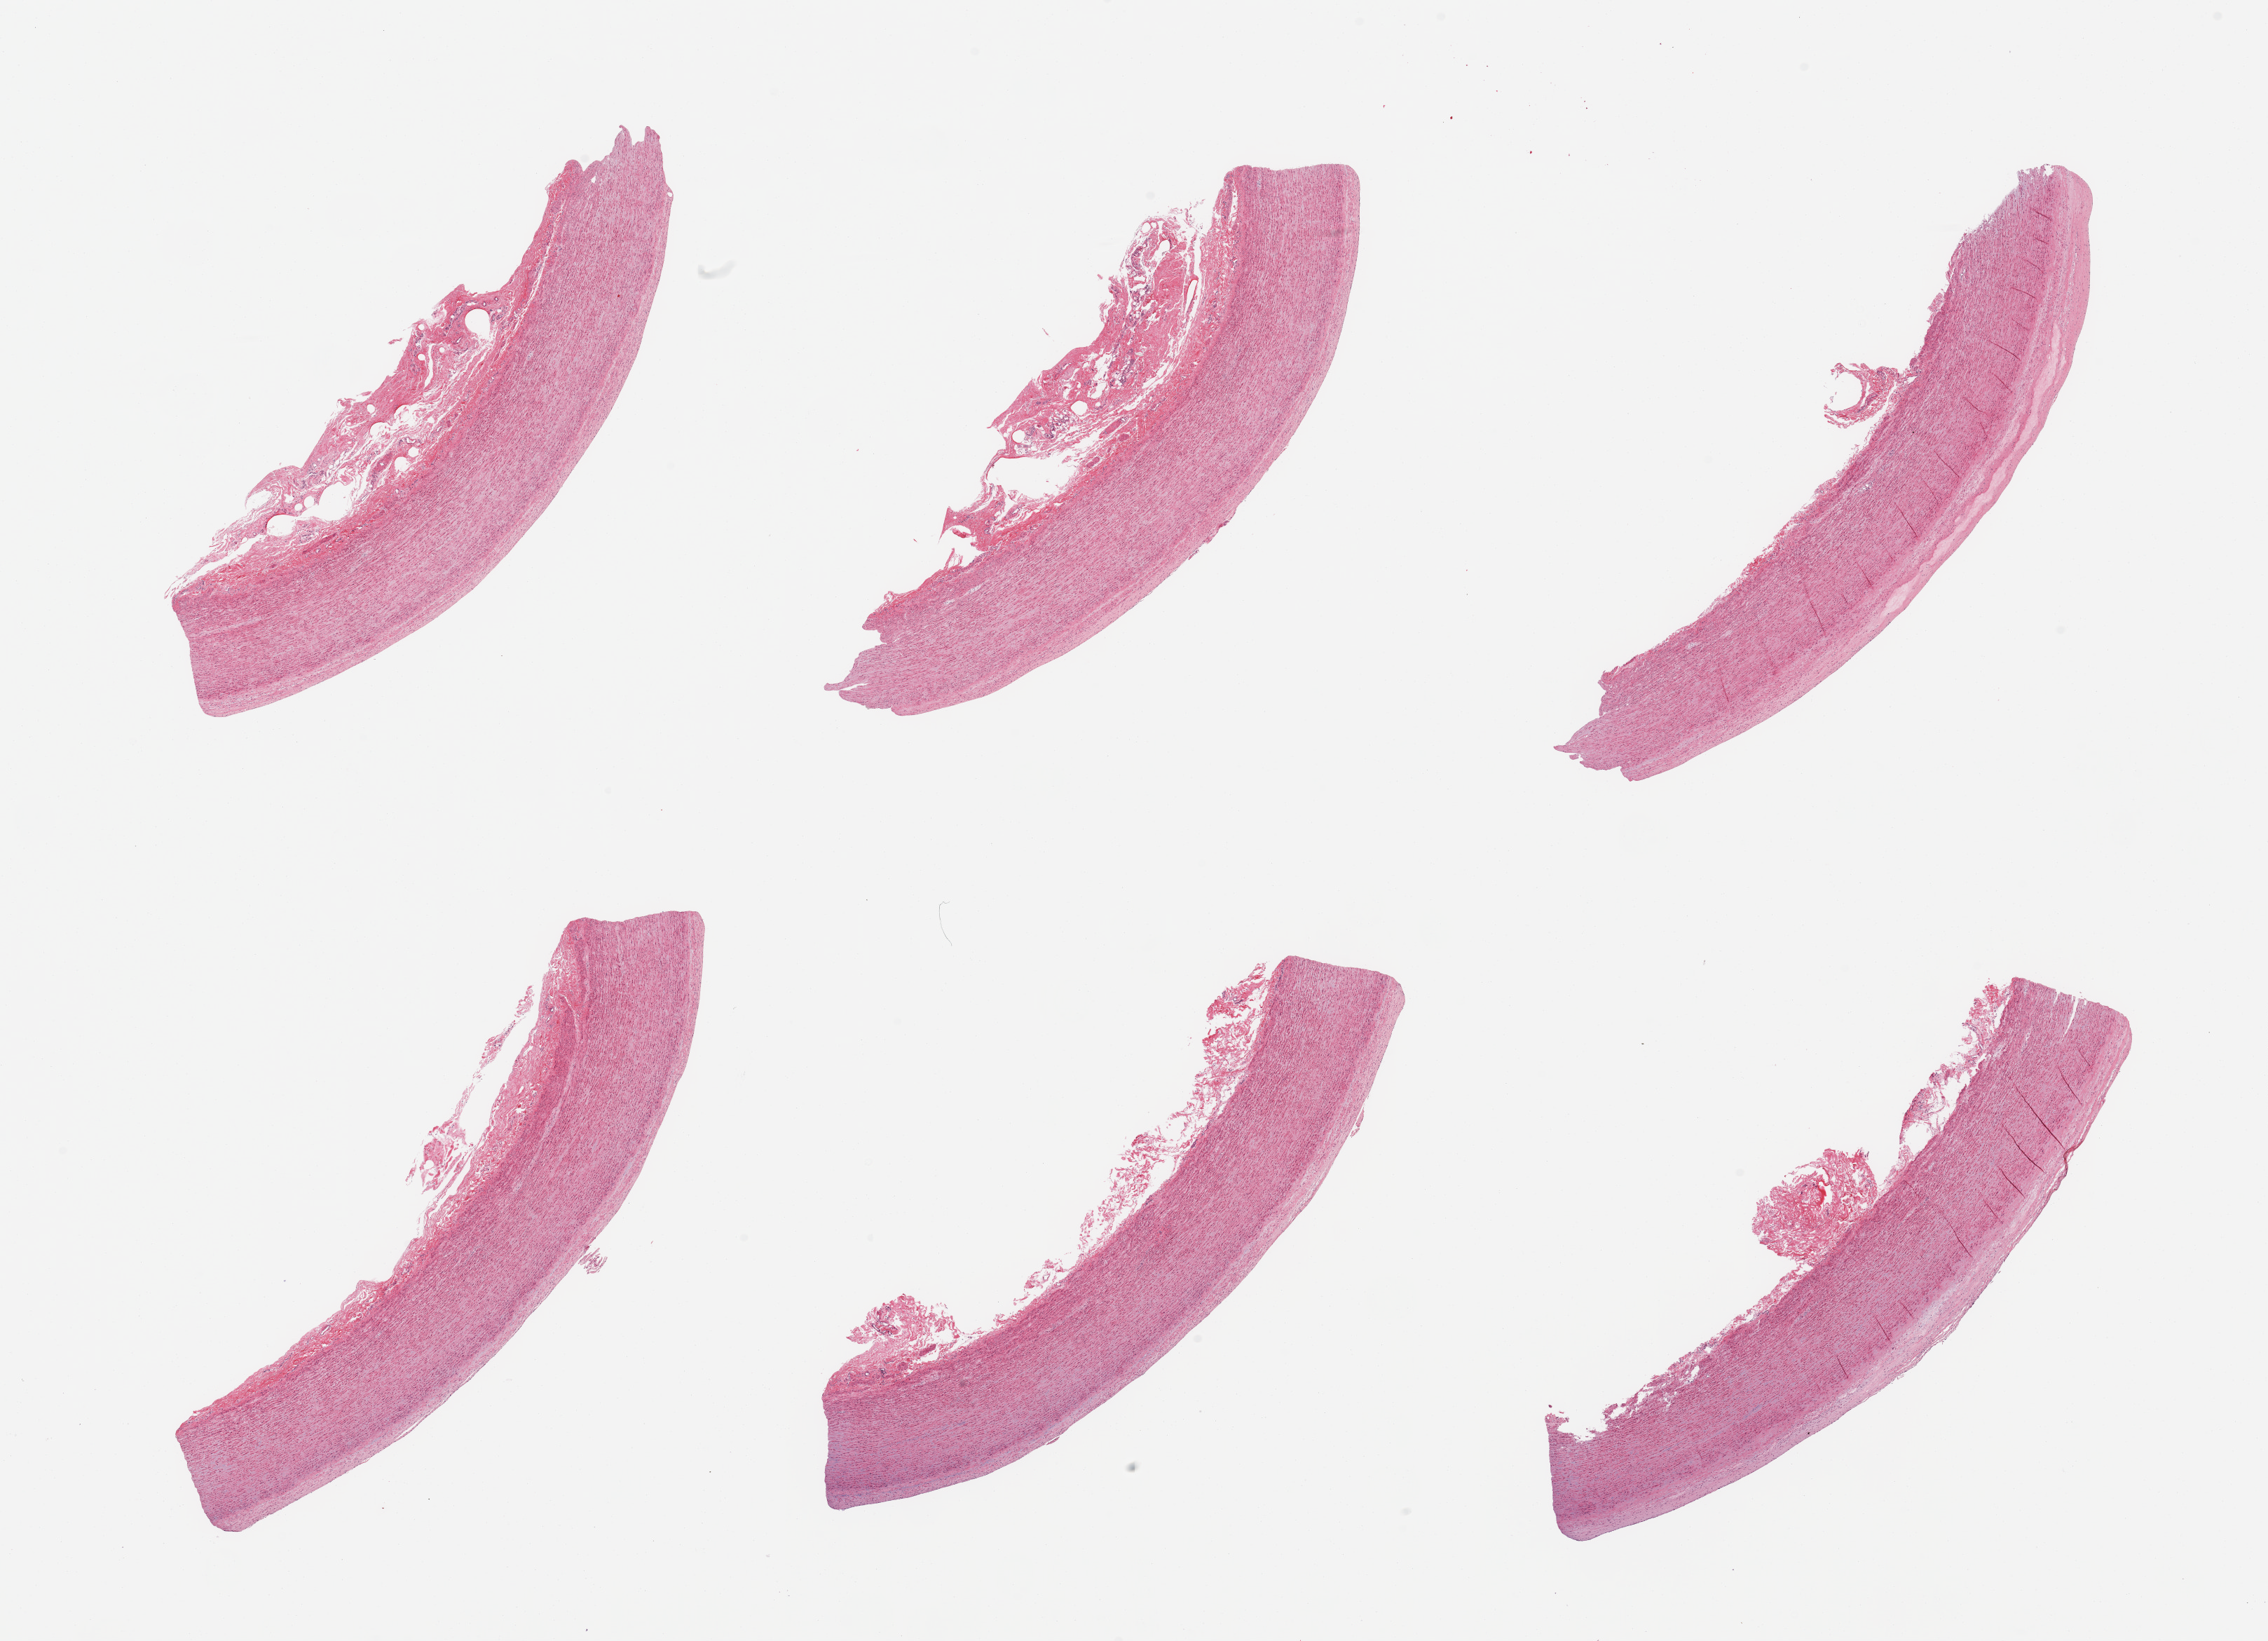
Haematoxylin and eosin whole-slide image, whole scanned area (about 25.6 x 18.5 mm) shown as a low-resolution overview, PAXgene-fixed paraffin-embedded (PFPE) section, section of aorta (target tissue), donor tissue sample. Donor sex: female.
Reviewer comment on this tissue sample: 6 pieces; flat plaques; up to 1 mm adherent adventitia.